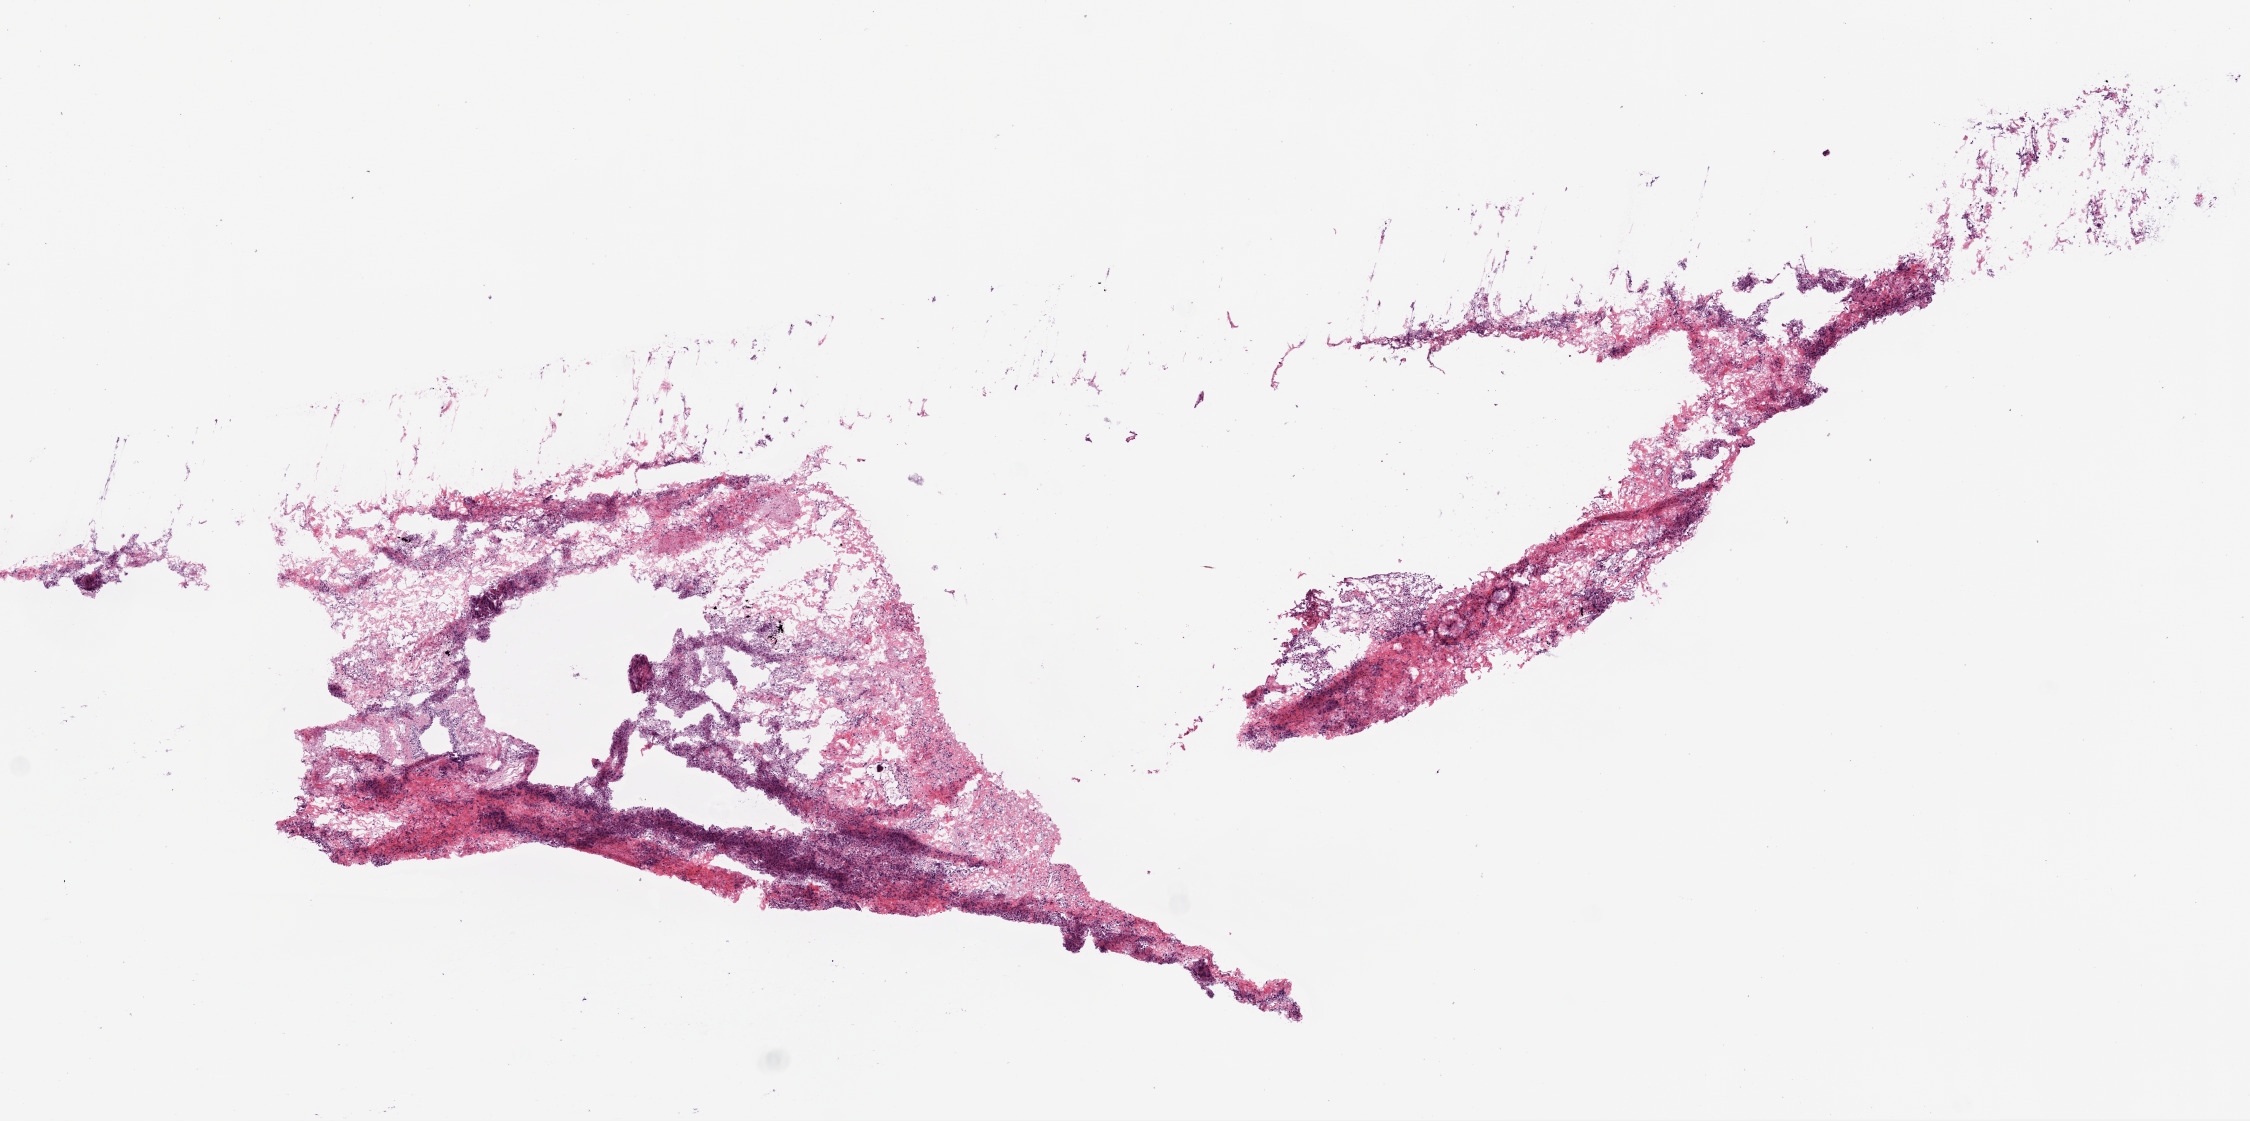
Digitized Hematoxylin and eosin (H&E) stained tissue section (whole slide) — low-resolution overview of the scanned area, about 9.0 x 4.5 mm (from a 20x scan); frozen section; solid tissue normal (non-tumour tissue) sample from the lung. Patient: male, age at initial diagnosis 72 years.
This section: solid tissue normal sample (biorepository sample class). Patient diagnosis: Squamous cell carcinoma, NOS (middle lobe, lung).